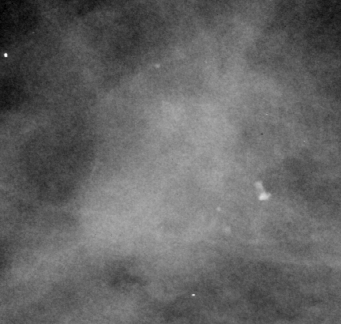
Region of interest cut from a scanned film mammogram (one marked finding), right breast, CC view.
- Mass, shape lobulated, margins obscured / ill defined; BI-RADS assessment category 3; pathology (as recorded): malignant.